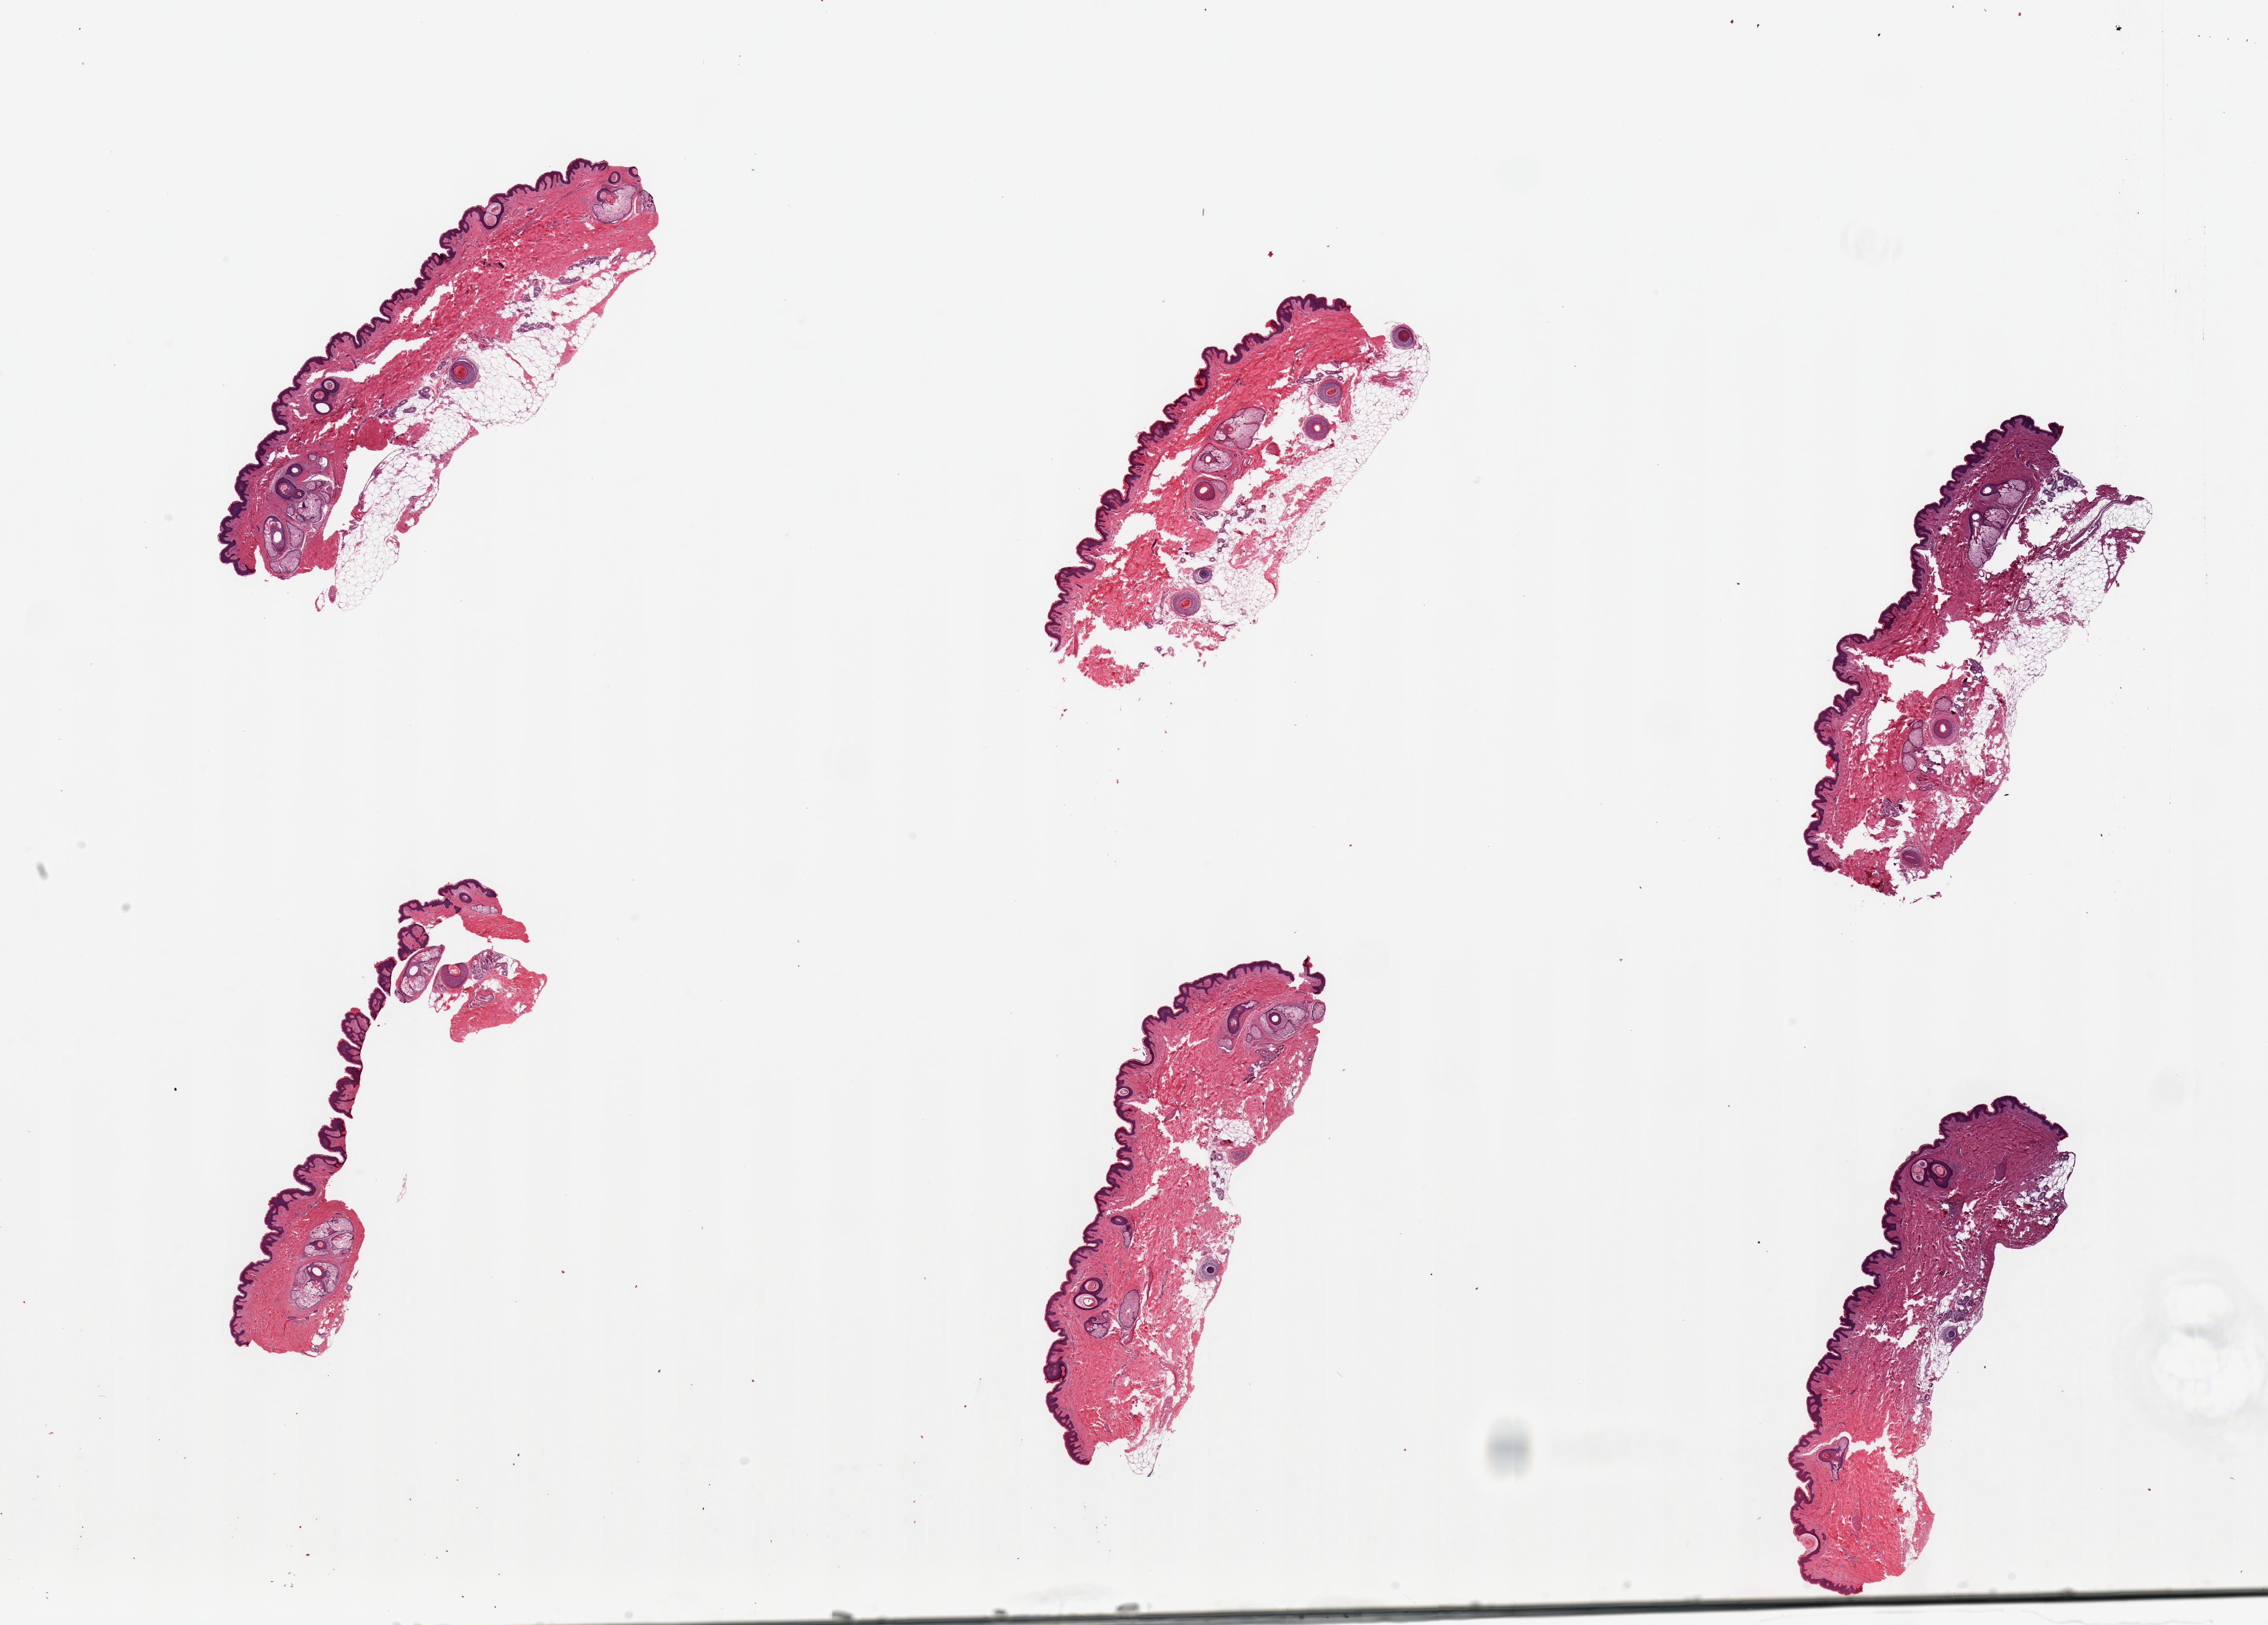
Whole-slide image, hematoxylin and eosin (H&E) stain, whole scanned area (about 29.5 x 21.2 mm, acquisition: 20x scan) shown as a low-resolution overview, PAXgene-fixed, paraffin-embedded tissue, target tissue: skin of suprapubic region, tissue donor sample. Male donor.
* pathologist's review note for this sample: 6 pieces ~7x2mm. Squamous epithelium is ~2-3% of thickness